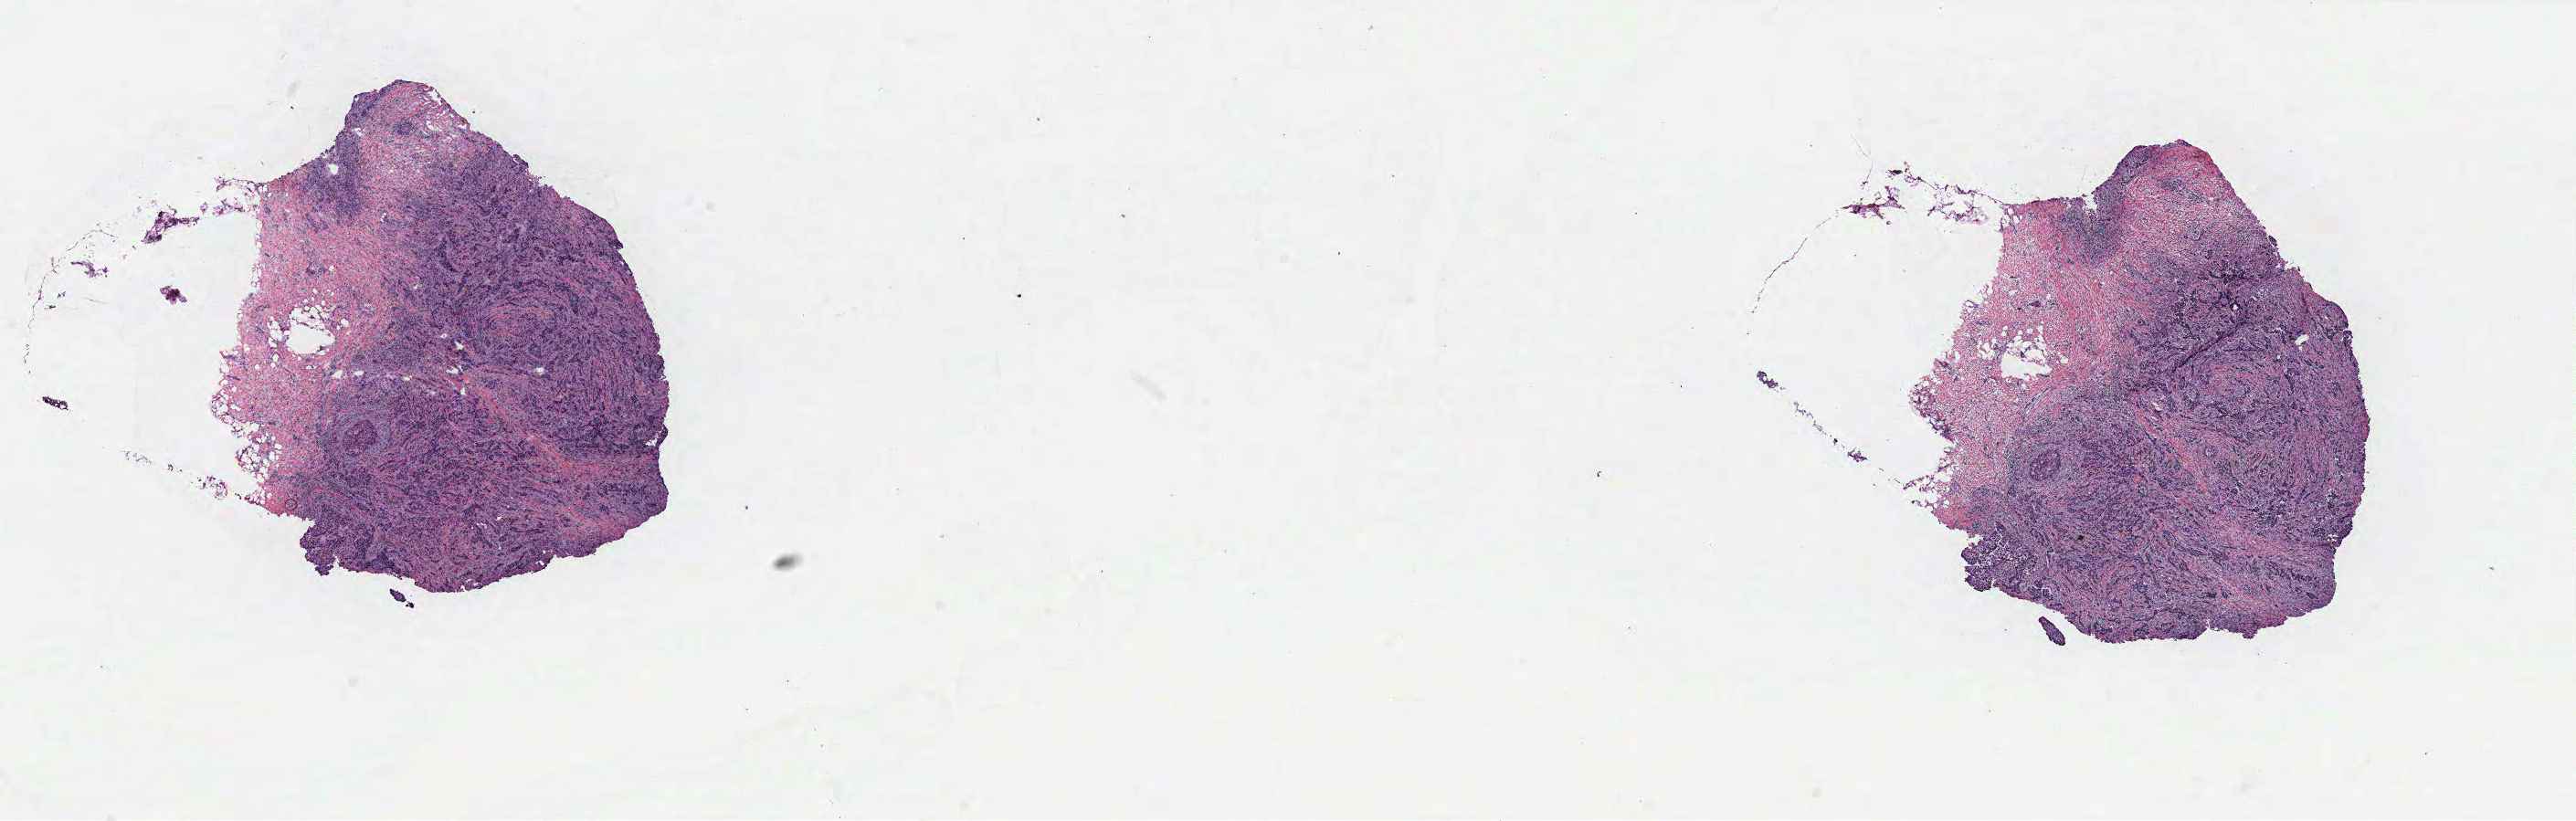
Whole-slide histology image, H&E-stained — a low-resolution overview of the entire scanned area, about 22.6 x 7.2 mm, breast, tissue type not recorded.
Patient diagnosis (cohort enrolment): breast cancer (breast).